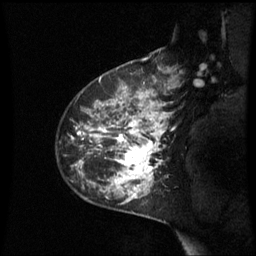
Breast MRI (dynamic contrast-enhanced), one sagittal slice; slice 43 of 60 in the series (ordered by position); dynamic contrast-enhanced series, image 2 of 3 at this slice position (ordered by acquisition); 1.5 T; TE 4.2 ms, TR 8.9 ms; 2.4 mm slice thickness; 256 × 256 image matrix. Patient: female, 42 years. From the clinical record (not read from this slice): setting: breast cancer imaged before/during neoadjuvant chemotherapy; receptor status: HER2-positive.
Structures marked on this image (semi-automatically segmented with operator editing):
- analysis volume of interest (the breast-tissue region the enhancement analysis was run in; not a lesion): bounding box (x1, y1, x2, y2) in pixels: (70, 93, 171, 210)
- tumour enhancement mask (voxels above the 70 % enhancement threshold inside the analysis volume of interest): (79, 93, 170, 198)